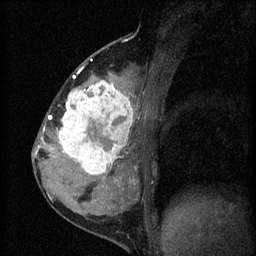
Breast MRI (dynamic contrast-enhanced), one sagittal slice. Slice 26 of 60 in the series (ordered by position). 3 images stored at this slice position (order not interpretable as contrast timing). 1.5 T. TE 4.2 ms, TR 8.2 ms. 2 mm slice thickness. 256 × 256 image matrix, field of view 180 × 180 mm. Female patient, age 37 years.
Outlined on this slice (semi-automatic segmentation, software-assisted and operator-edited):
- analysis volume of interest (the breast-tissue region the enhancement analysis was run in; not a lesion): box from (x=53, y=78) to (x=139, y=181) px
- tumour enhancement mask (voxels above the 70 % enhancement threshold inside the analysis volume of interest): (x=56, y=78)–(x=133, y=179)